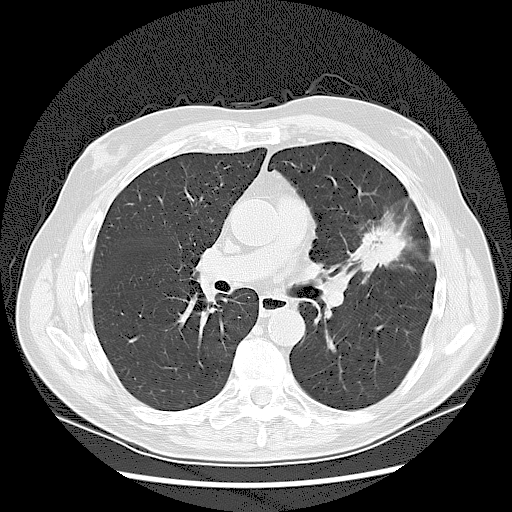
Axial slice from a low-dose chest CT screening exam. Baseline annual screen. Lung window (W 1500 / L -600 HU). Slice 60 of 132 in the series. 512 × 512 image matrix. Male participant, aged 65 years at enrolment.
Expert reader's lesion annotation, box from (x=348, y=223) to (x=398, y=269) px. The exam's reader record, not a measurement of the box and not confirmed to be the same lesion: non-calcified nodule or mass ≥4 mm, left upper lobe, 37 × 27 mm, spiculated (stellate) margins, soft tissue attenuation. Official screen result: positive, change unspecified: nodule(s) >= 4 mm or enlarging nodule(s), mass(es), or other non-specific abnormalities suspicious for lung cancer.